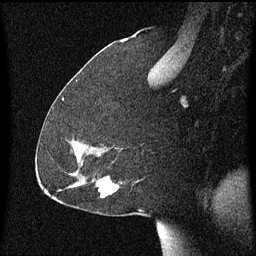
Breast MRI (dynamic contrast-enhanced), one sagittal slice. Slice 34 of 60 in the series (ordered by position). Dynamic contrast-enhanced series, image 2 of 3 at this slice position (ordered by acquisition). 1.5 T. TE 4.2 ms, TR 8.4 ms. 256 × 256 image matrix, field of view 200 × 200 mm. Female patient, age 59 years.
Structures marked on this image (semi-automatic segmentation, software-assisted and operator-edited):
- analysis volume of interest (the breast-tissue region the enhancement analysis was run in; not a lesion): bounding box (x1, y1, x2, y2) in pixels: (92, 178, 119, 199)
- tumour enhancement mask (voxels above the 70 % enhancement threshold inside the analysis volume of interest): (98, 178, 119, 197)